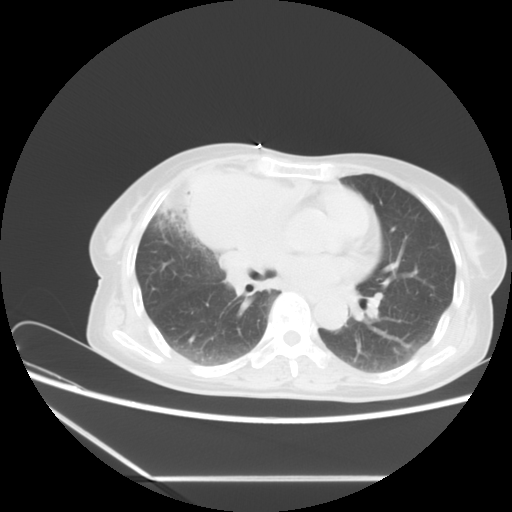
Chest CT, one axial slice. Slice 5 of 16 in the series (ordered by position). Lung window (W 1500 / L -600 HU). 5 mm slice thickness. 512 × 512 image matrix, field of view 350 × 350 mm. Patient: female, 63 years. Case-level facts recorded for this patient, not image findings: clinical TNM (as recorded): T2b N1 M0.
Outlined on this slice (bounding box drawn by a radiologist):
- lung tumour (recorded histology: adenocarcinoma): bounding box (x1, y1, x2, y2) in pixels: (172, 146, 316, 253)